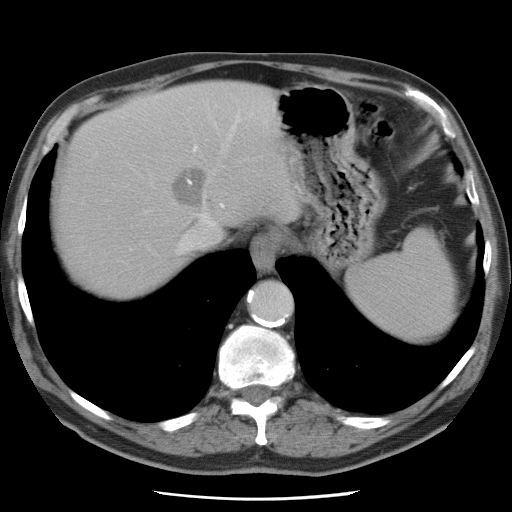
Contrast-enhanced abdominal CT, one axial slice. Position 65 of 78 along the scan axis. 120 kVp. Intravenous contrast given. Soft-tissue window (W 400 / L 40 HU). 5 mm slice thickness. 512 × 512 image matrix, field of view 337 × 337 mm. Male patient, age 75 years. Case-level facts recorded for this patient, not image findings: diagnosis: colorectal cancer liver metastases, imaged before liver resection; multiple liver metastases: yes; largest metastasis: 2.4 cm; disease in both lobes: yes.
Outlined on this slice (manually delineated by an expert):
- hepatic veins: bounding box <175,114,249,255> (left, top, right, bottom; pixels)
- liver: <59,81,299,300>
- planned liver remnant (the part of the liver to remain after resection): <59,139,187,300>
- liver metastasis: <171,168,207,208>